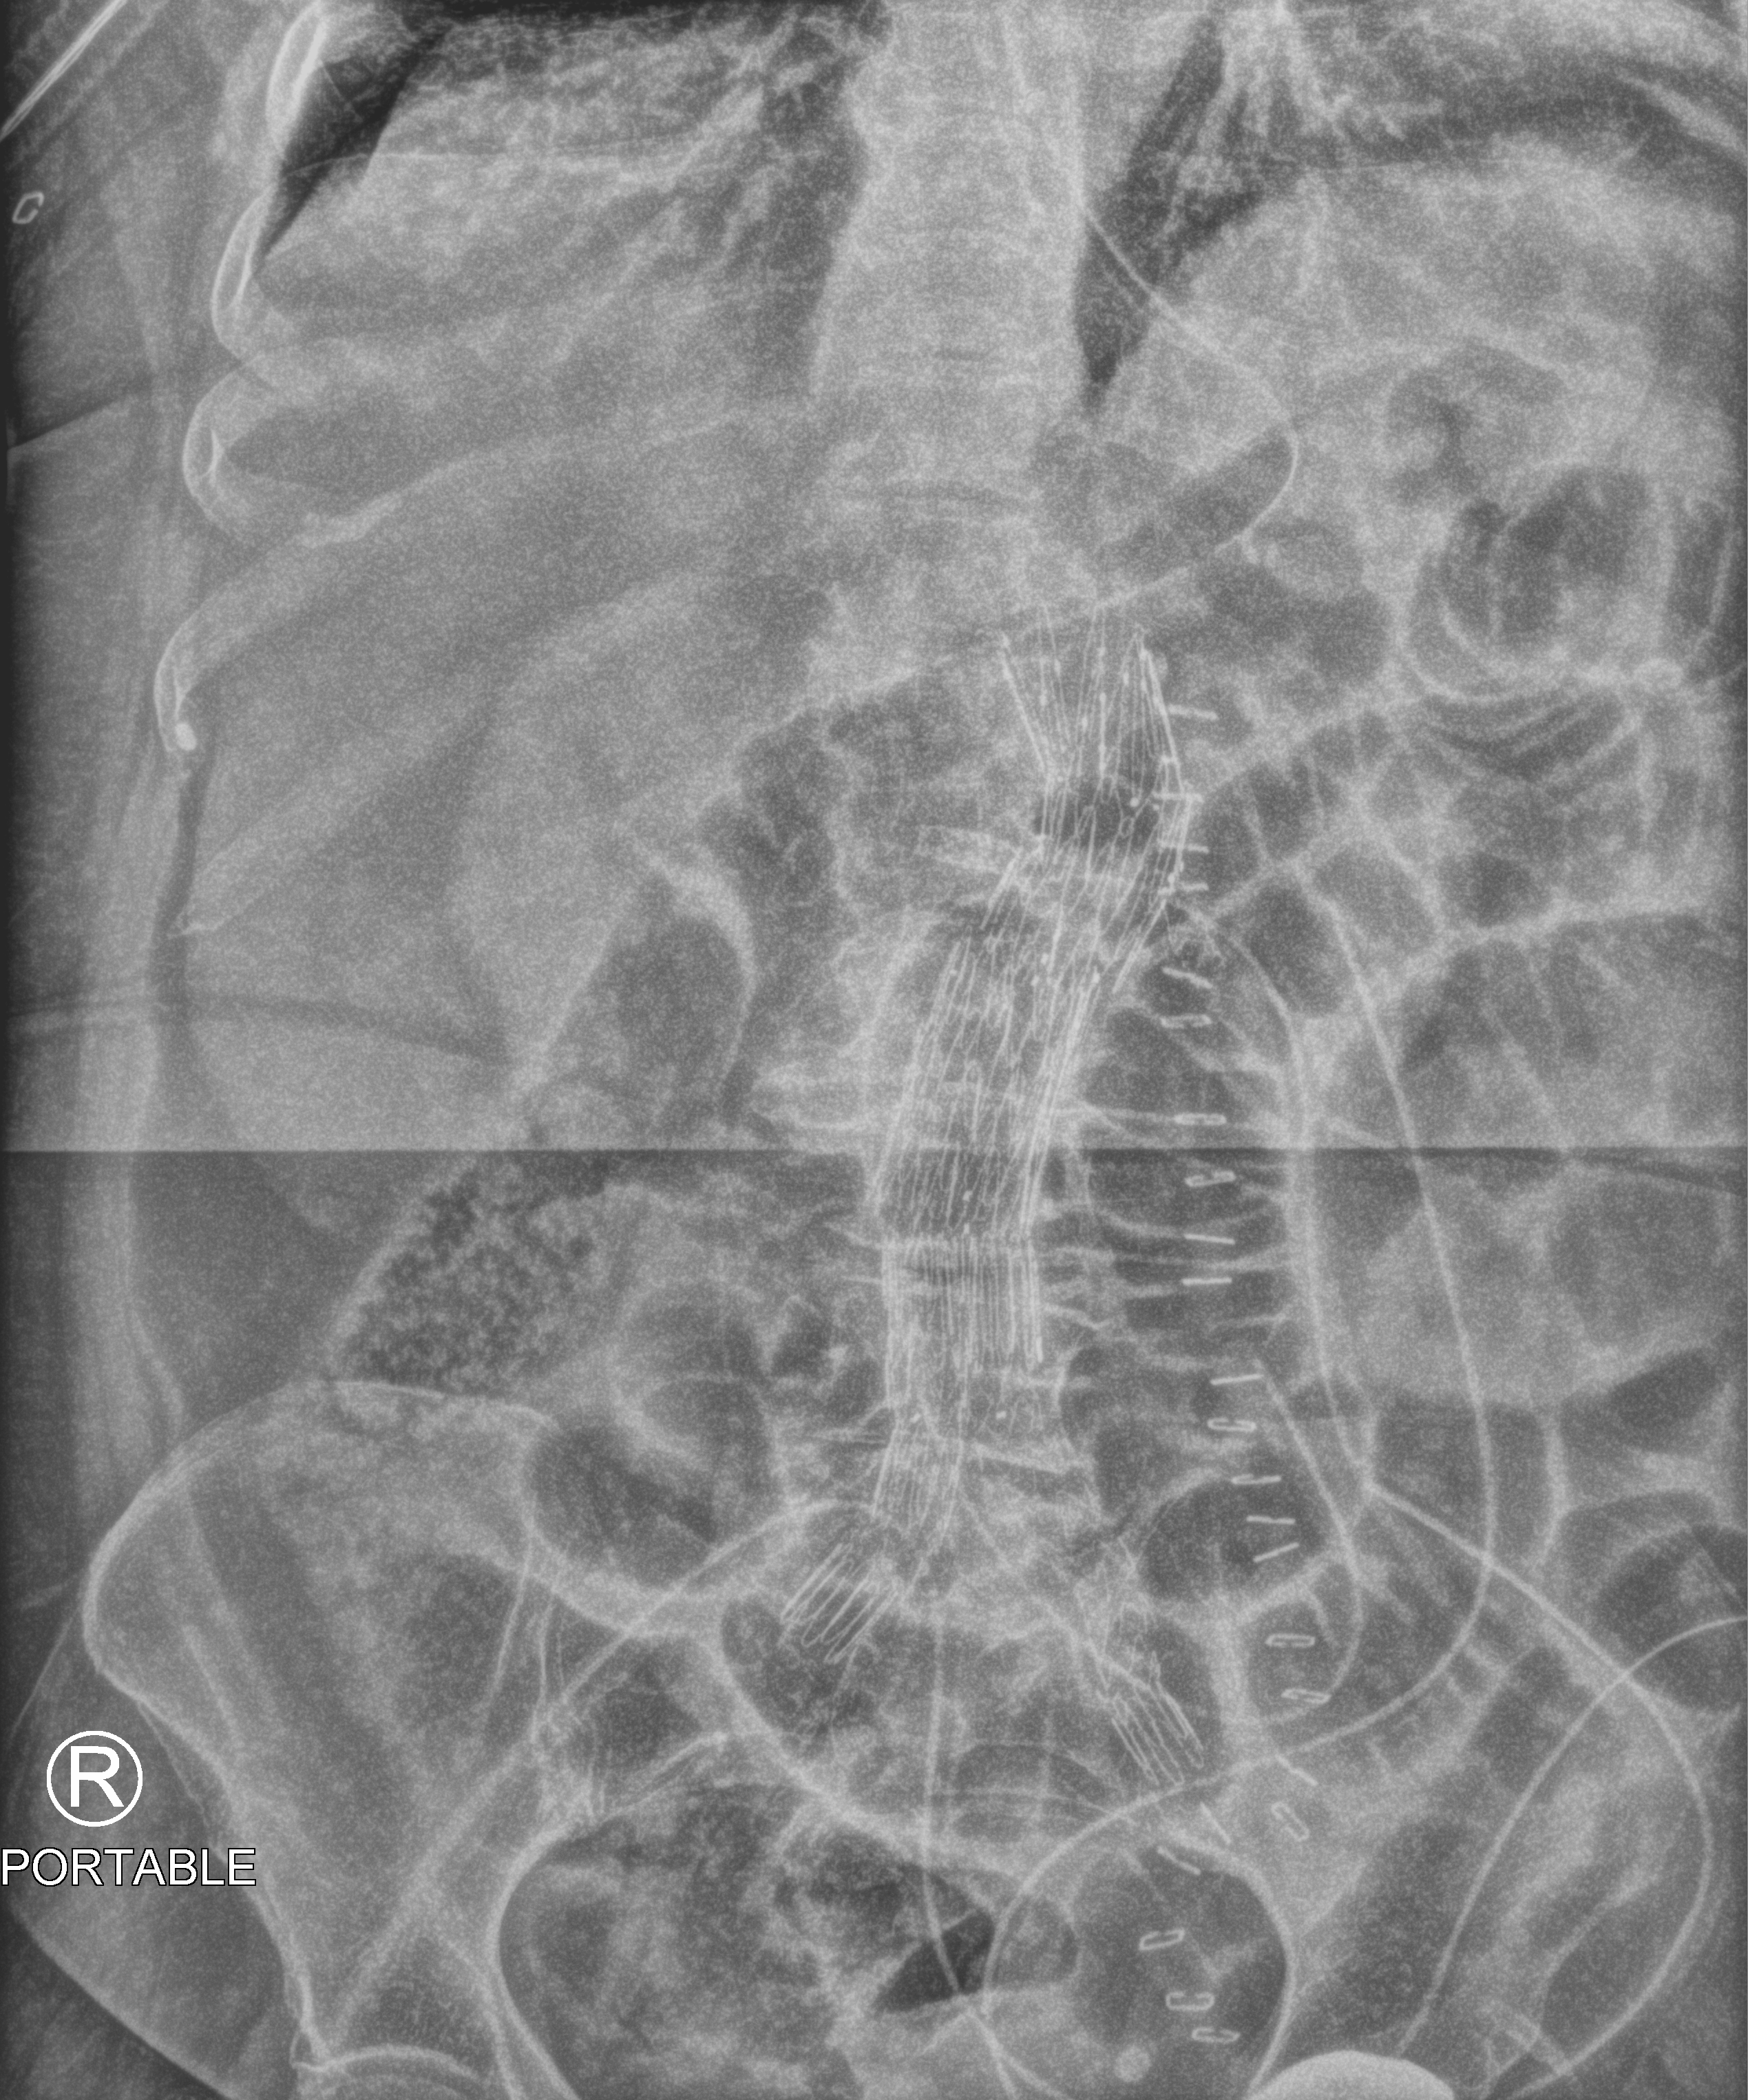
Abdomen X-ray (portable). Female patient hospitalised with COVID-19, age 60–74 years.
Admission-level facts for this patient (not findings on this image; timing relative to this image not recorded):
- mechanically ventilated during this hospital stay: no
- admitted to intensive care during this hospital stay: yes